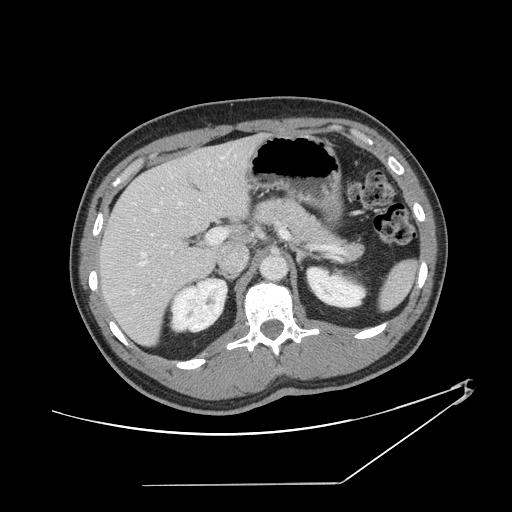
Contrast-enhanced abdominal CT, one axial slice. Position 83 of 152 along the scan axis. Reconstruction kernel STANDARD. 120 kVp. Intravenous contrast given. Soft-tissue window (W 400 / L 40 HU). 2.5 mm slice thickness. 512 × 512 image matrix. Male patient, age 45 years. From the clinical record (not read from this slice): diagnosis: colorectal cancer liver metastases, imaged before liver resection; multiple liver metastases: no; largest metastasis: 1 cm; disease in both lobes: no.
Outlined on this slice (expert manual segmentation):
- hepatic veins: box from (x=111, y=156) to (x=225, y=294) px
- liver: (x=101, y=136)–(x=260, y=345)
- planned liver remnant (the part of the liver to remain after resection): (x=101, y=156)–(x=217, y=345)
- portal vein (with intrahepatic branches): (x=139, y=229)–(x=289, y=266)